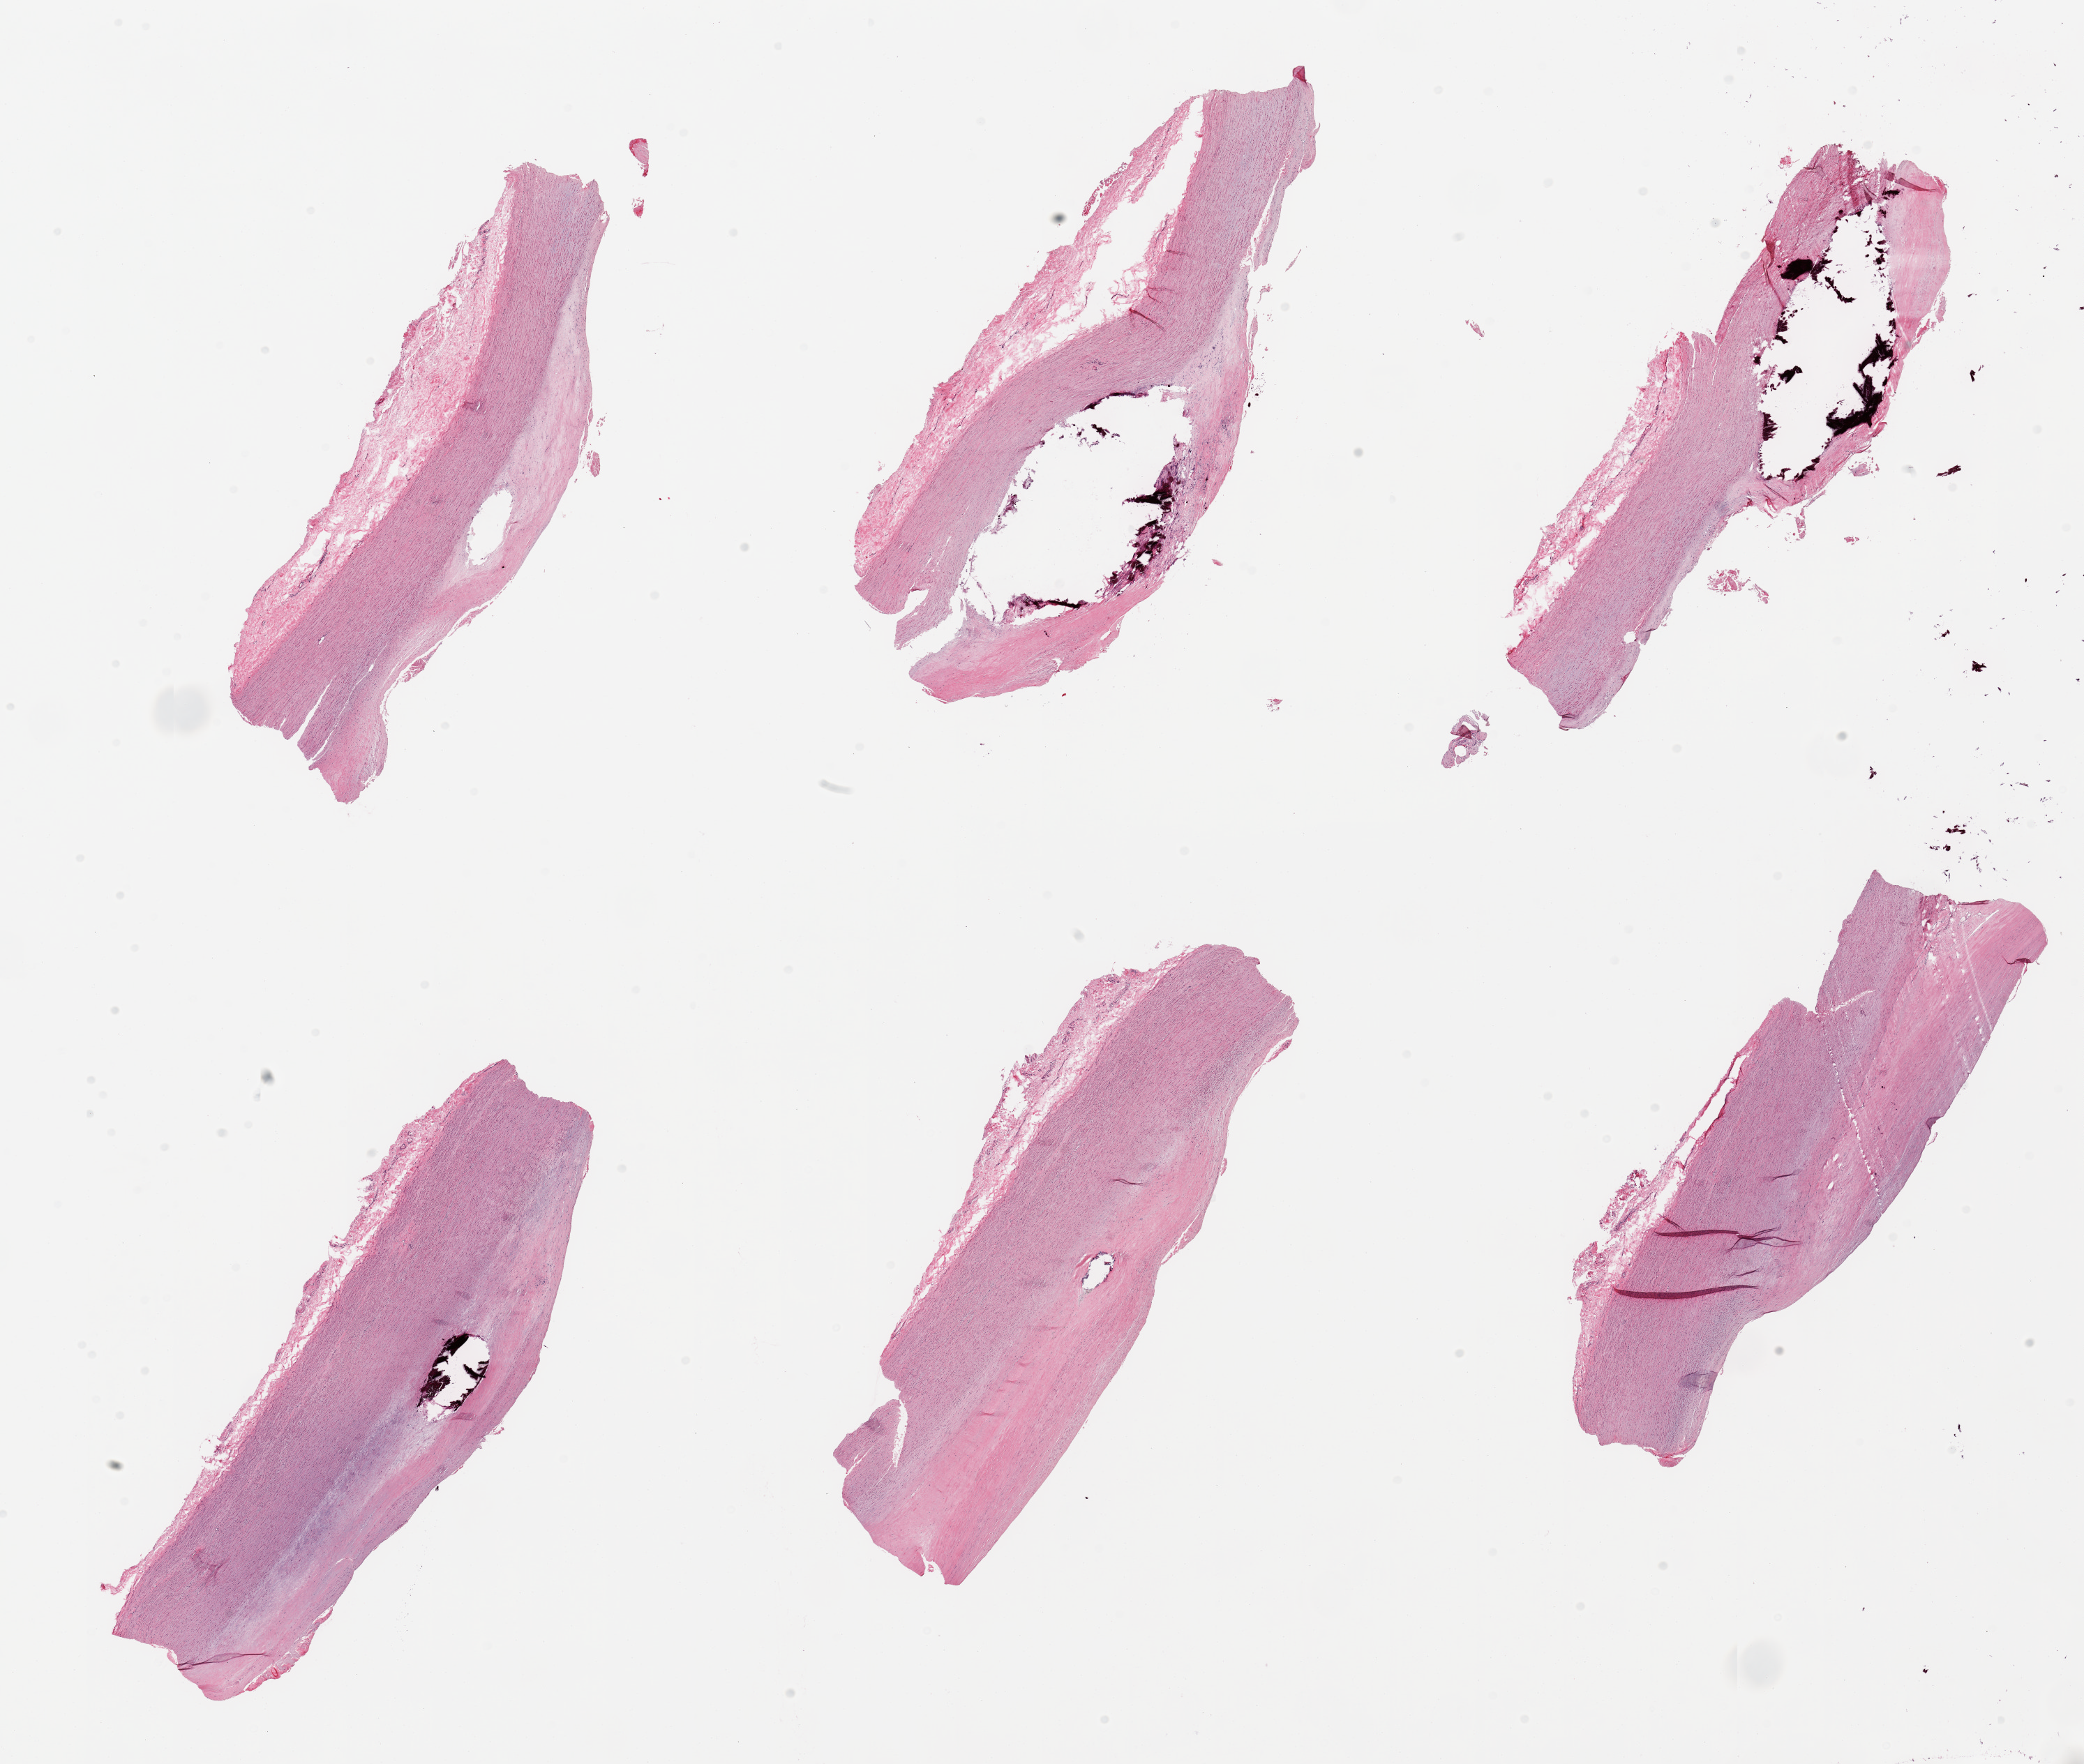
Whole-slide image, hematoxylin and eosin (H&E) stain — whole scanned area (about 23.6 x 20.0 mm, slide scanned at 20x) shown as a low-resolution overview, PAXgene-fixed paraffin-embedded (PFPE) section, section of aorta (target tissue), donor tissue sample. Donor: female.
• reviewer comment on this tissue sample: 6 pieces pronounced focally calcifying atherosis up to ~1.4mm